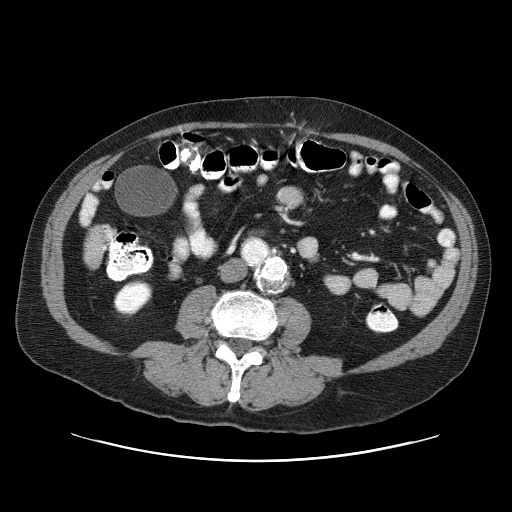
Contrast-enhanced abdominal CT (liver protocol), one axial slice. Slice 1 of 87 in the series (ordered by position). 120 kVp. One of 3 acquisitions stored at this slice position. Soft-tissue window (W 400 / L 40 HU). 512 × 512 image matrix. From the clinical record (not read from this slice): diagnosis: hepatocellular carcinoma (patient treated with transarterial chemoembolisation; whether this scan precedes or follows treatment is not stated here); TNM stage (as recorded): Stage-IIIA; Child-Pugh class: A; tumour differentiation: well differentiated; tumour nodularity: multinodular.
Structures marked on this image (semi-automatically segmented with operator editing):
- liver parenchyma outside the tumour (the mass and vessels are separate outlines, so this box may not span the whole liver): bounding box (x1, y1, x2, y2) in pixels: (80, 194, 104, 266)
- liver vessels: (82, 196, 96, 223)